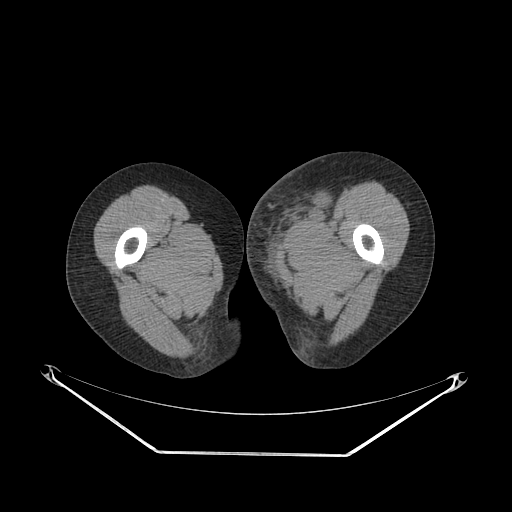
CT of an extremity soft-tissue mass (from a PET/CT study), one axial slice; slice 44 of 267 in the series (ordered by position); 140 kVp; soft-tissue window (W 400 / L 40 HU); 512 × 512 image matrix, field of view 500 × 500 mm. Female patient. Case-level facts recorded for this patient, not image findings: histological type: leiomyosarcoma; grade: high; site of the primary tumour: groin.
Outlined on this slice (expert contour drawn on MRI and transferred to this co-registered scan by the dataset authors):
- gross tumour volume including surrounding oedema: bounding box <244,176,330,254> (left, top, right, bottom; pixels)
- gross tumour volume (mass): <299,194,327,215>